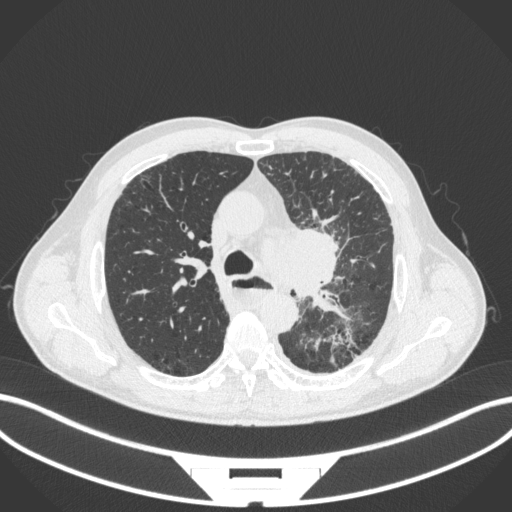
Chest CT, one axial slice; position 261 of 411 along the scan axis; lung window (W 1500 / L -600 HU); 1 mm slice thickness; 512 × 512 image matrix, field of view 400 × 400 mm. Male patient, age 57 years. Case-level facts recorded for this patient, not image findings: clinical TNM (as recorded): T2a N1 M0.
Outlined on this slice (rectangle marked by the reading radiologist):
- lung tumour (recorded histology: squamous cell carcinoma): bounding box <266,218,353,306> (left, top, right, bottom; pixels)